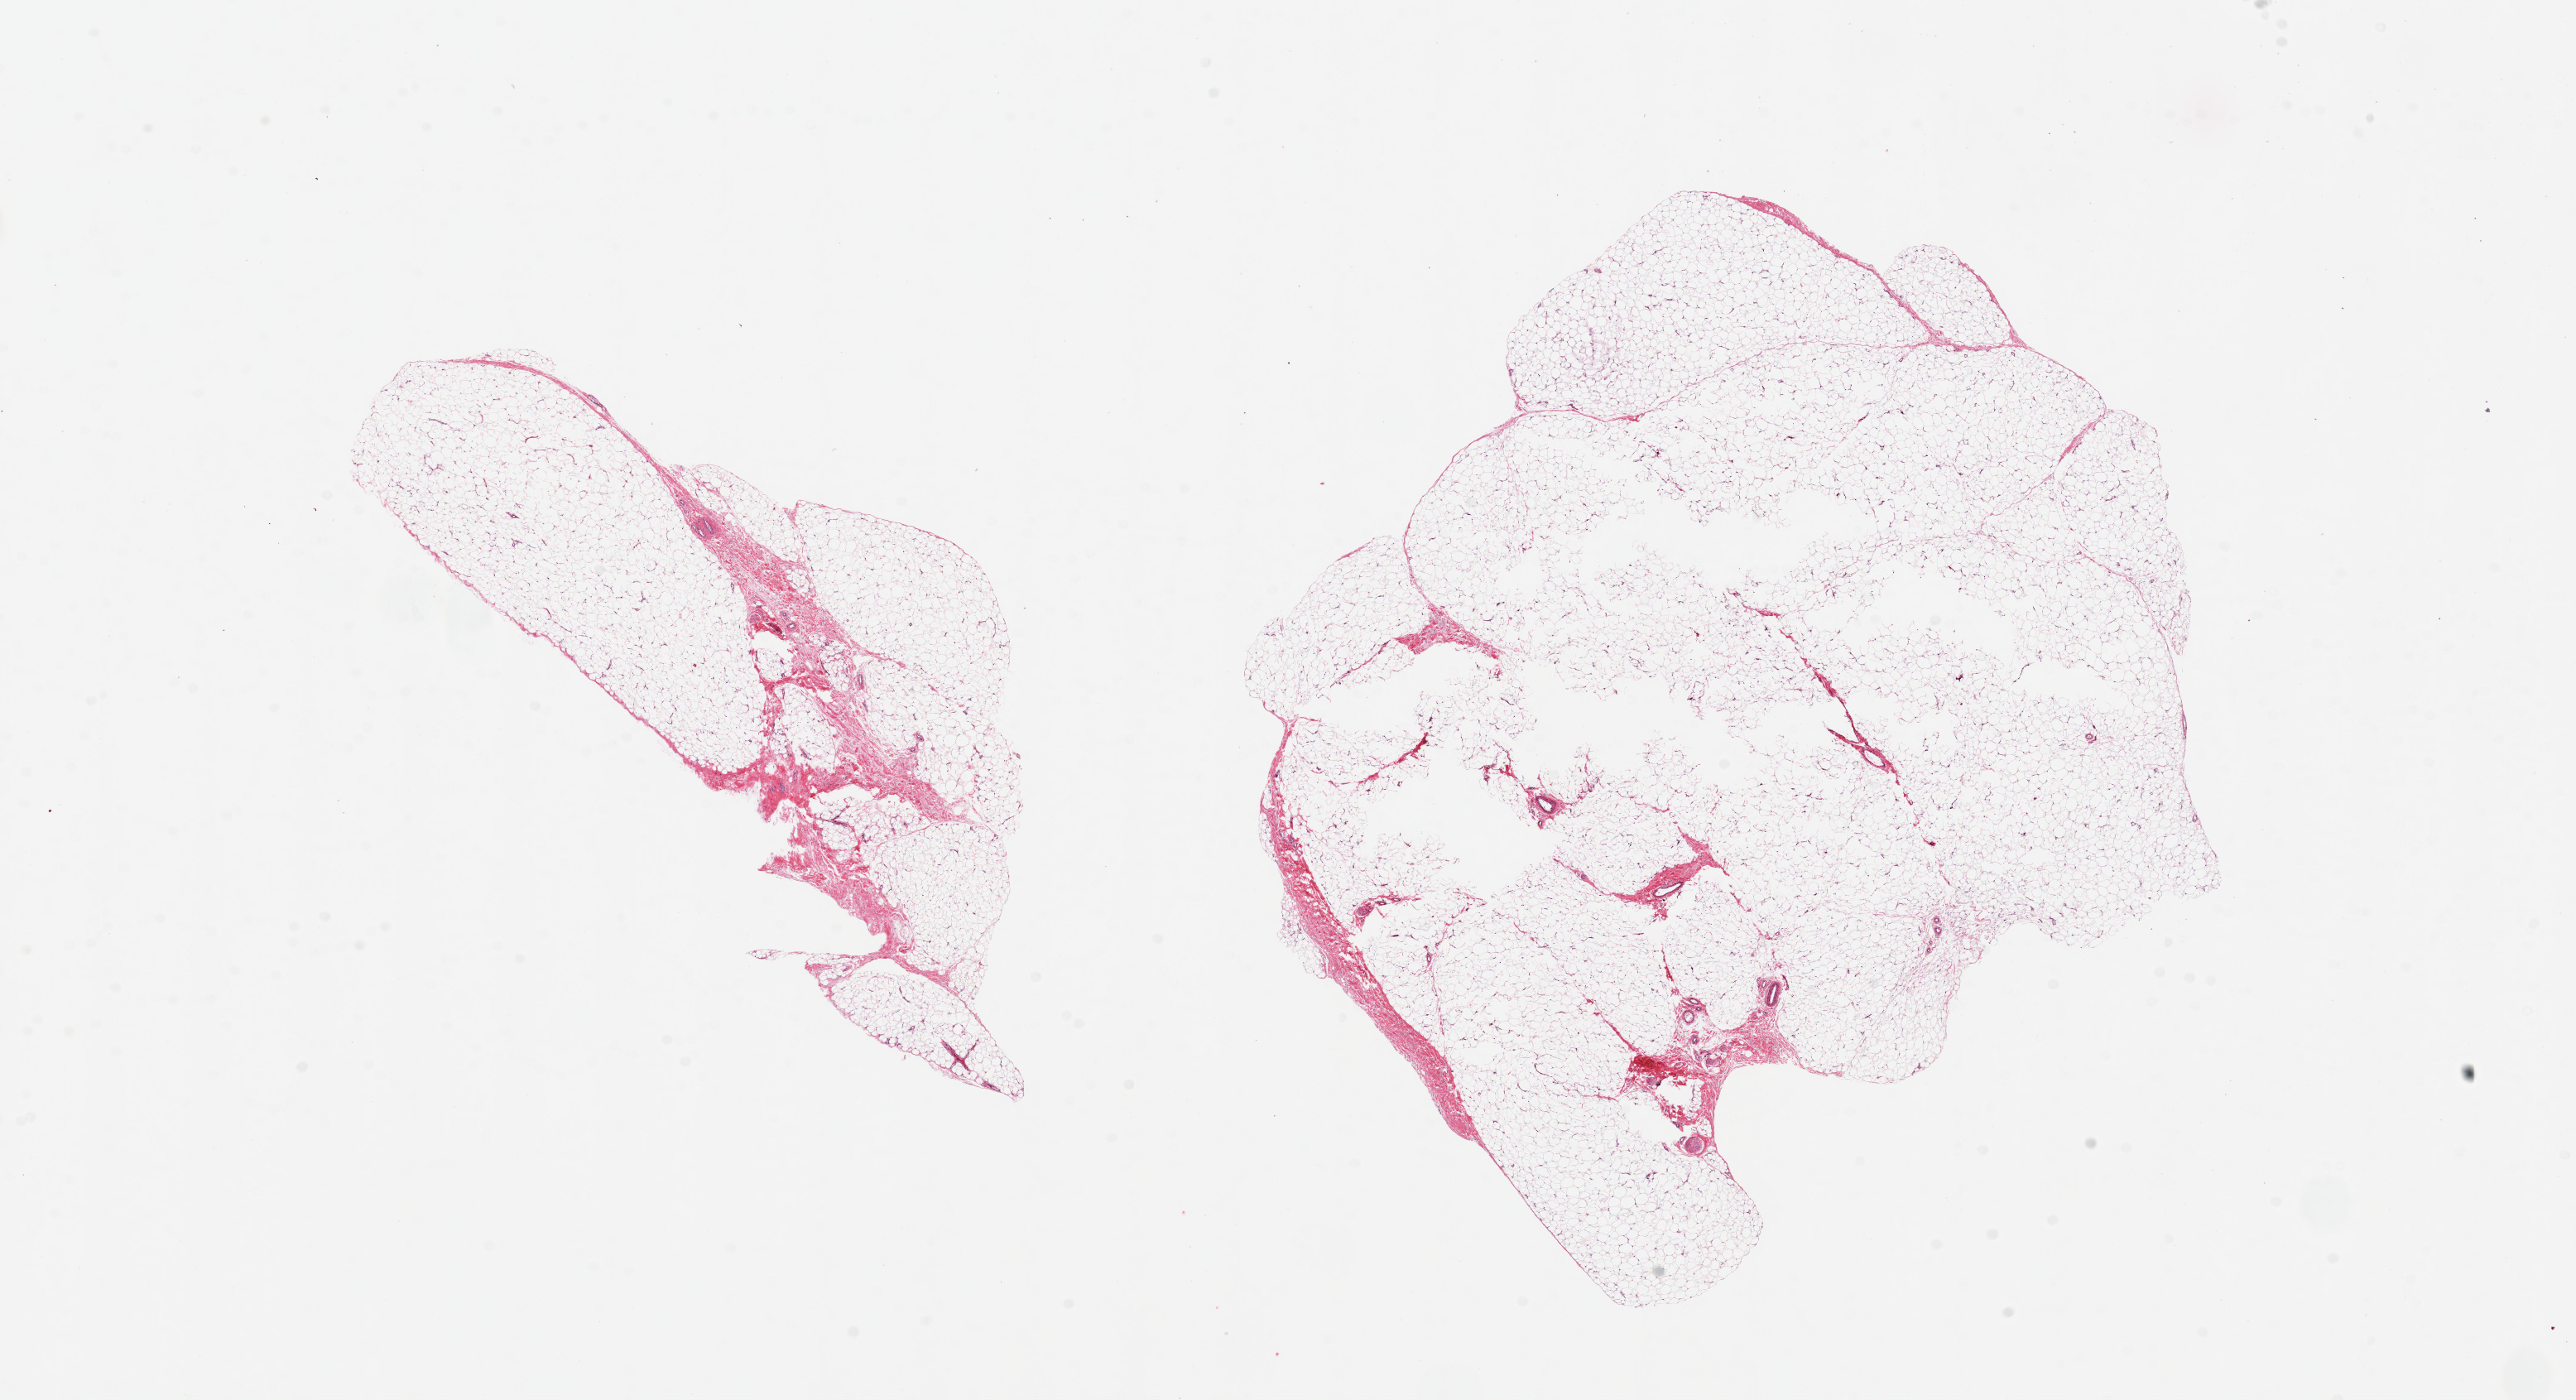
Hematoxylin and eosin (H&E) whole-slide image — a low-resolution overview of the entire scanned area, about 24.6 x 13.4 mm (from a 20x scan), PAXgene-fixed, paraffin-embedded tissue, section of adipose tissue (target tissue), donor tissue sample. Donor: male.
Pathologist's review note for this sample: 2 pieces ~8x6mm.